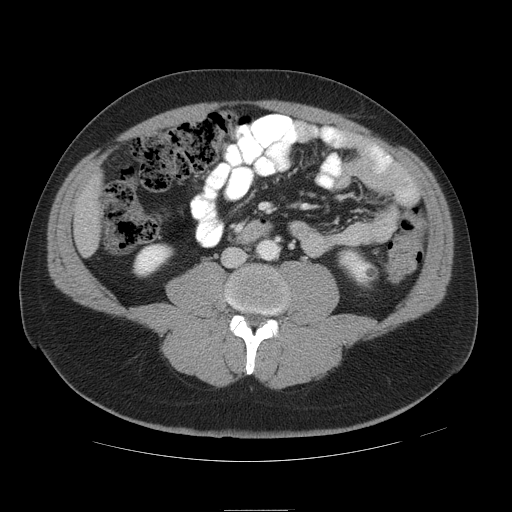
Contrast-enhanced abdominal CT, one axial slice; slice 10 of 49 in the series (ordered by position); intravenous contrast given; soft-tissue window (W 400 / L 40 HU); 5 mm slice thickness; 512 × 512 image matrix. Male patient, age 52 years. From the clinical record (not read from this slice): diagnosis: colorectal cancer liver metastases, imaged before liver resection; multiple liver metastases: yes; largest metastasis: 5.1 cm; disease in both lobes: yes.
Outlined on this slice (expert manual segmentation):
- liver: bounding box <76,181,100,254> (left, top, right, bottom; pixels)